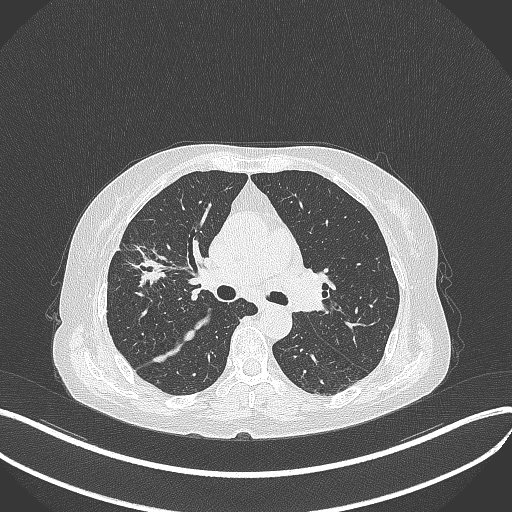
Chest CT, one axial slice. Position 243 of 429 along the scan axis. 120 kVp. Lung window (W 1500 / L -600 HU). 1 mm slice thickness. 512 × 512 image matrix, field of view 400 × 400 mm. Patient: female, 69 years. From the clinical record (not read from this slice): clinical TNM (as recorded): T1b N3 M0.
Annotated regions visible in this slice (bounding box drawn by a radiologist):
- lung tumour (recorded histology: small cell carcinoma): bounding box [x1, y1, x2, y2] px = [123, 243, 171, 293]